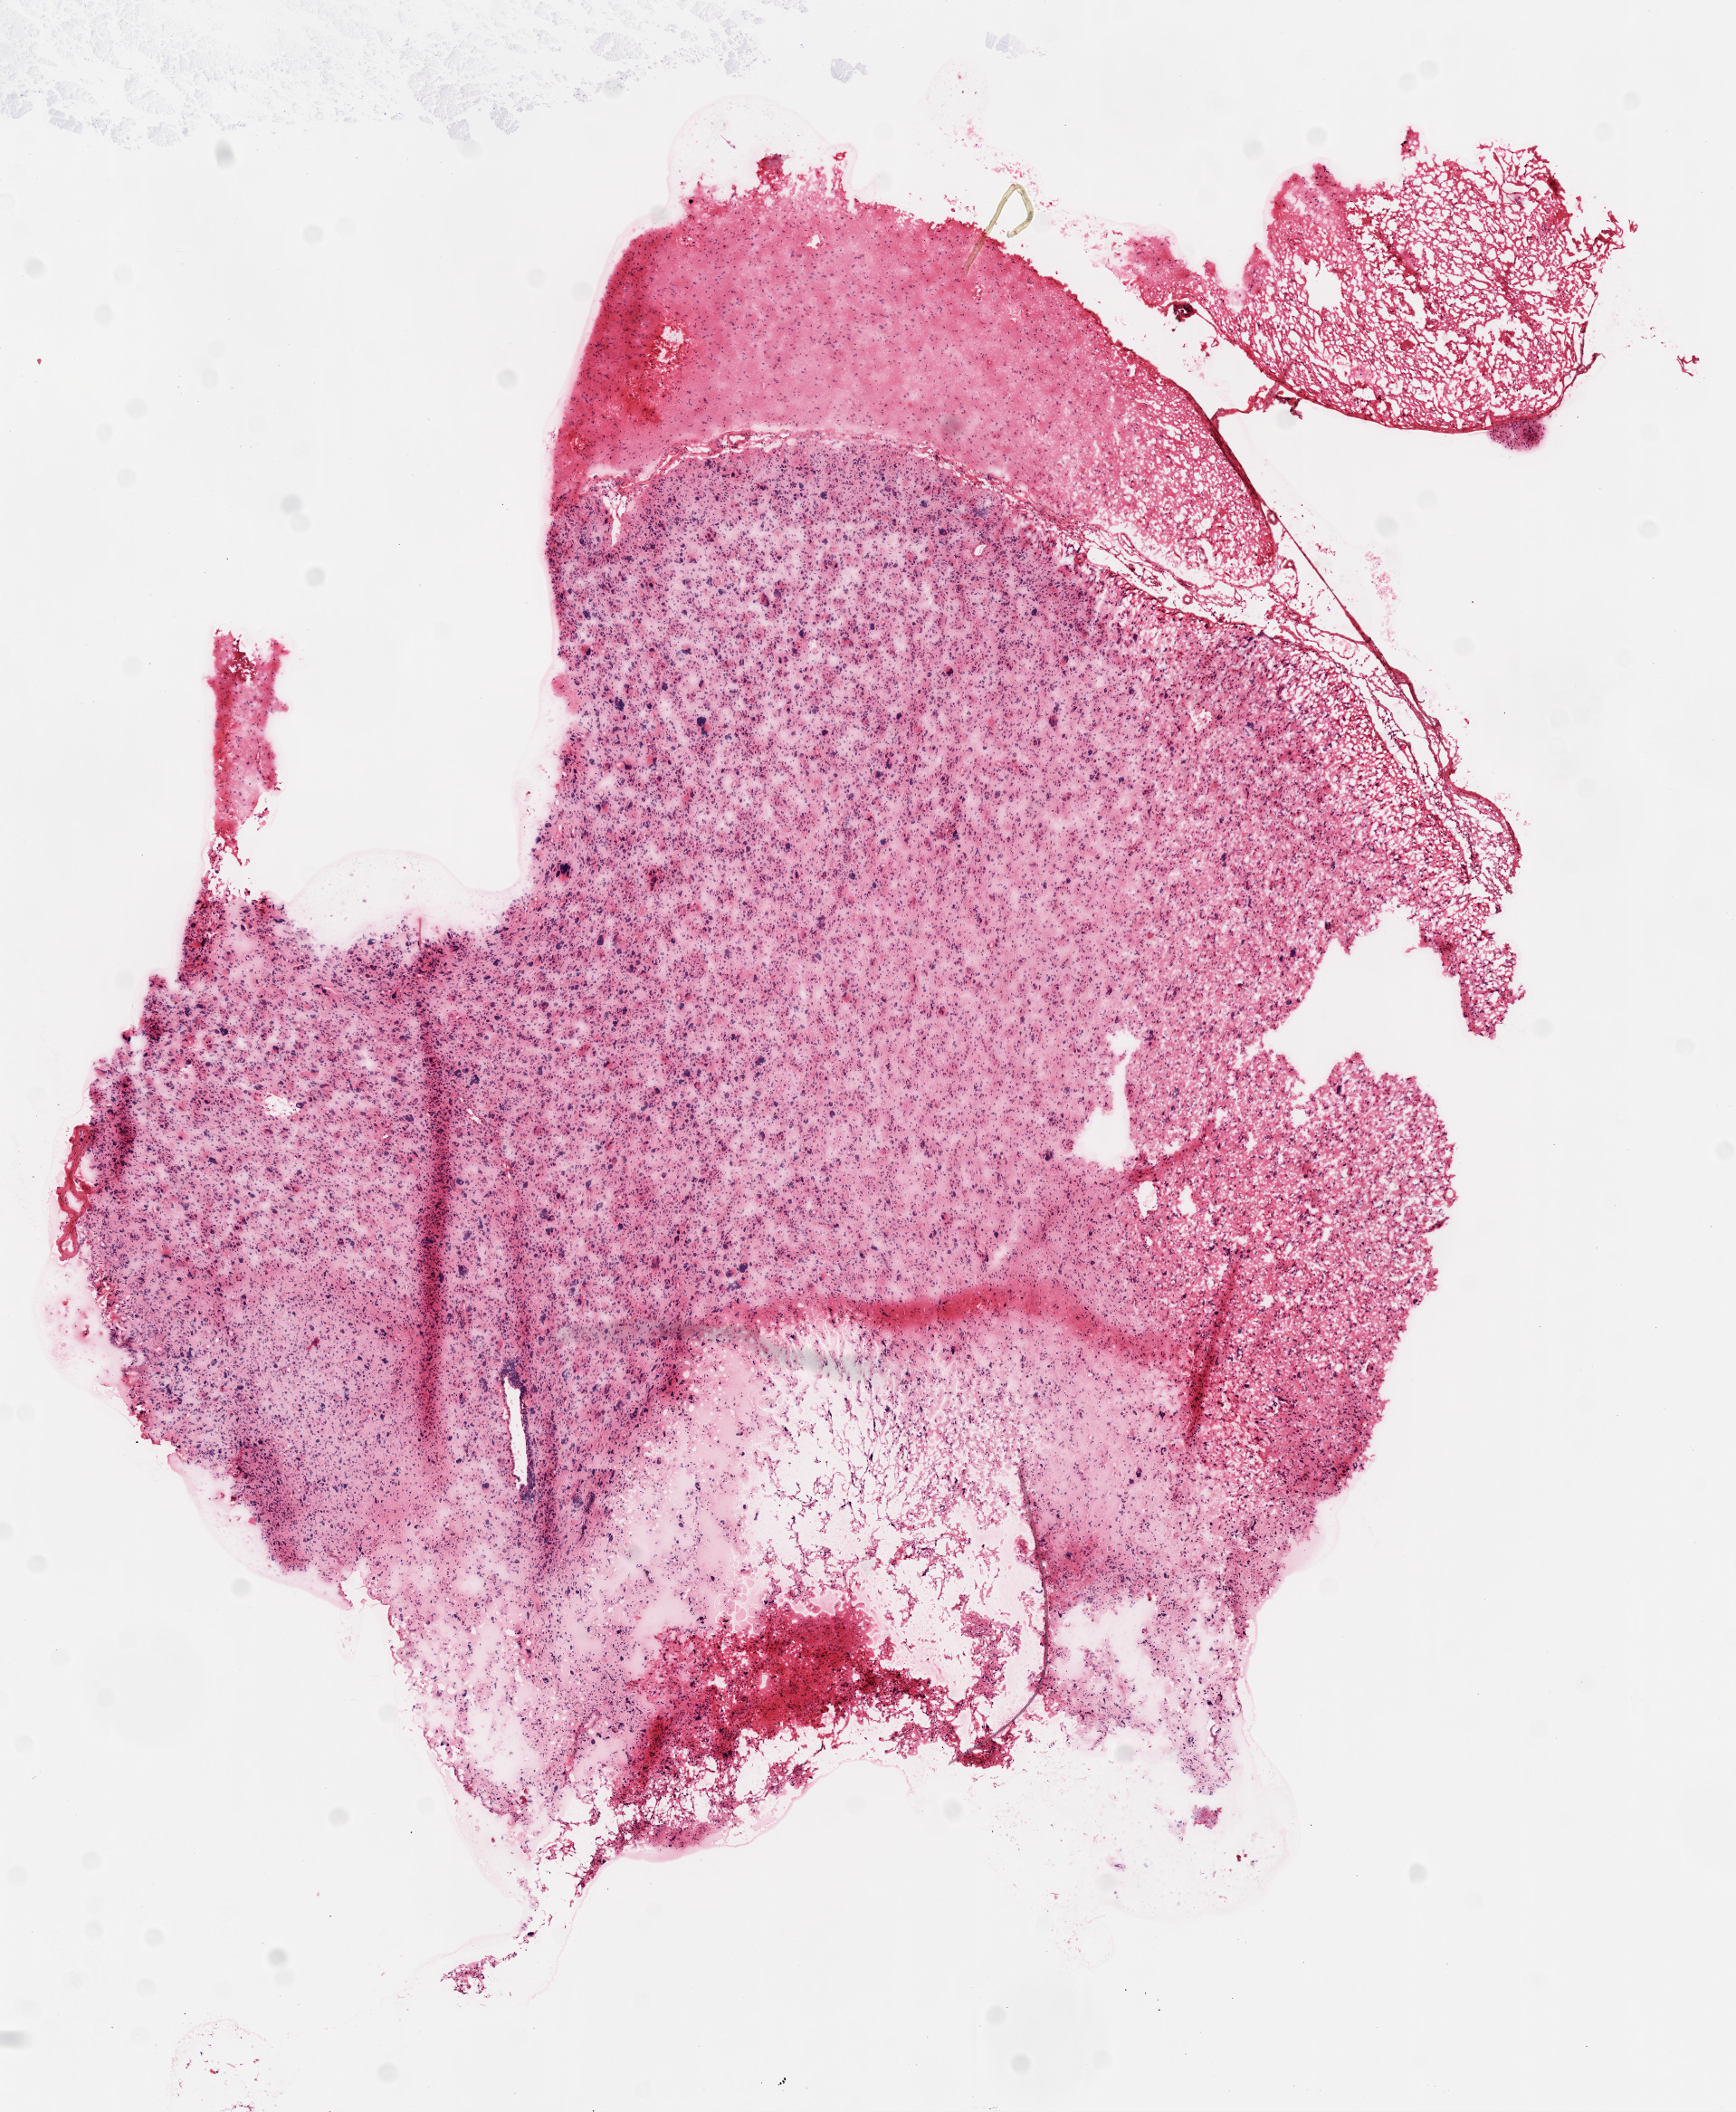
Whole-slide histology image, H&E-stained — low-resolution overview of the scanned area, about 7.7 x 9.4 mm (acquisition: 20x scan). Frozen section from the top of the tissue portion. Brain, primary tumour sample. Patient: male, age at initial diagnosis 46 years. Pathologist review of this section (percent, as recorded): tumour cells 75%, tumour nuclei 85%, normal cells 0%, stromal cells 10%, necrosis 15%.
- diagnosis: Glioblastoma